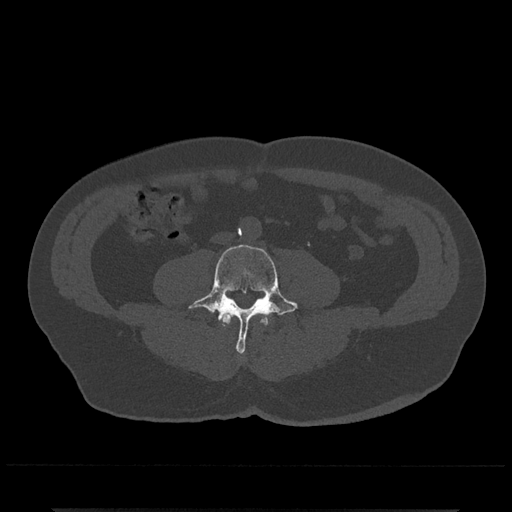
CT including the spine, one axial slice; slice 157 of 797 in the series (ordered by position); reconstruction kernel Br40s/3; bone window (W 1800 / L 400 HU); 0.5 mm slice thickness; 512 × 512 image matrix, field of view 393 × 393 mm. Patient: male, 67 years. Case-level facts recorded for this patient, not image findings: primary cancer: prostate.
Structures marked on this image (semi-automatic segmentation, software-assisted and operator-edited):
- L3 vertebra: bounding box [x1, y1, x2, y2] px = [220, 312, 269, 327]
- L4 vertebra: [188, 244, 298, 354]